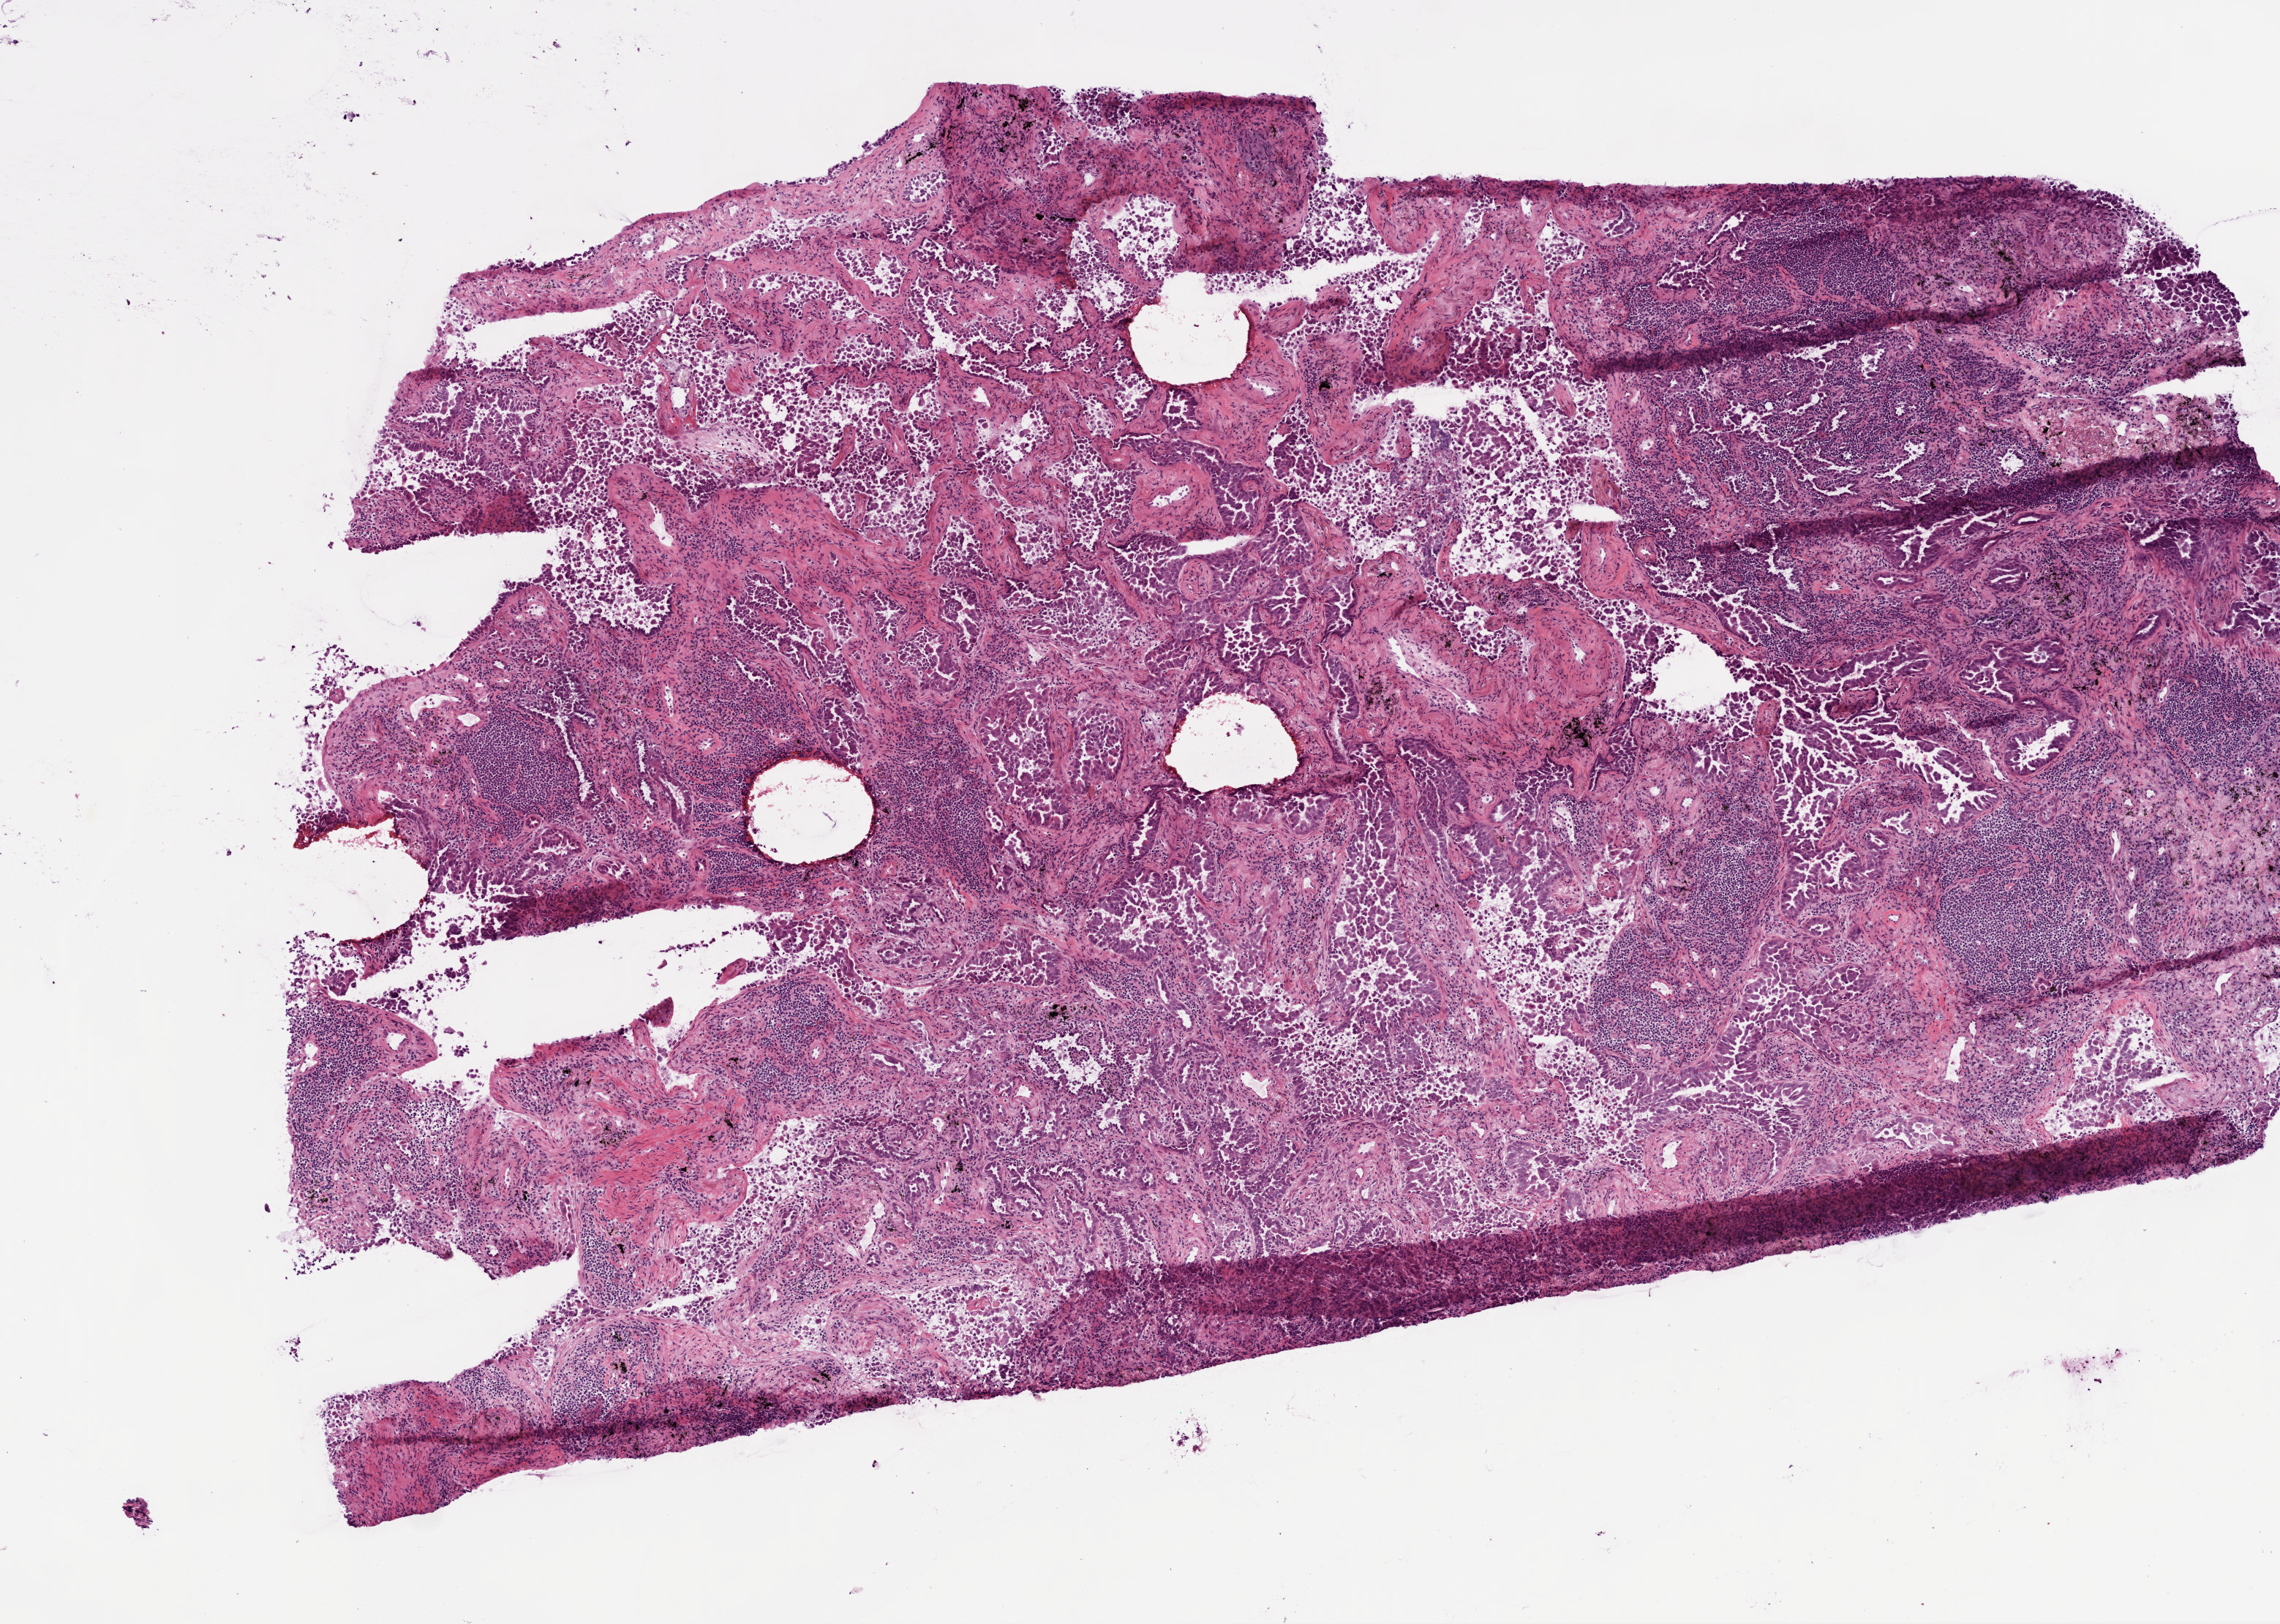
Digitized H&E tissue section (whole slide) — whole scanned area (about 6.3 x 4.5 mm, from a 20x scan) shown as a low-resolution overview. Frozen section from the top of the tissue portion. Primary tumour sample from the lung. Patient: female, age at initial diagnosis 72 years. Slide review estimates, as recorded: tumour cells 60%, tumour nuclei 70%, normal cells 0%, stromal cells 25%, necrosis 15%.
Laterality: right. TNM: T1 N0 M0. Pathologic diagnosis: Adenocarcinoma, NOS (upper lobe, lung). AJCC pathologic stage: IA.